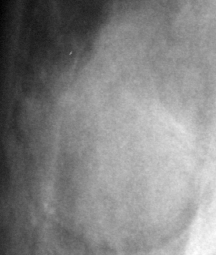
Cropped region of a digitized screen-film mammogram centred on a radiologist-marked abnormality, right breast, CC view, BI-RADS breast density category 3 (scale 1–4).
Marked abnormality: mass, shape round, margins circumscribed; BI-RADS assessment category 3; subtlety rating 5 on a 1 (subtle) to 5 (obvious) scale; pathology result (as recorded, not read from the image): benign.